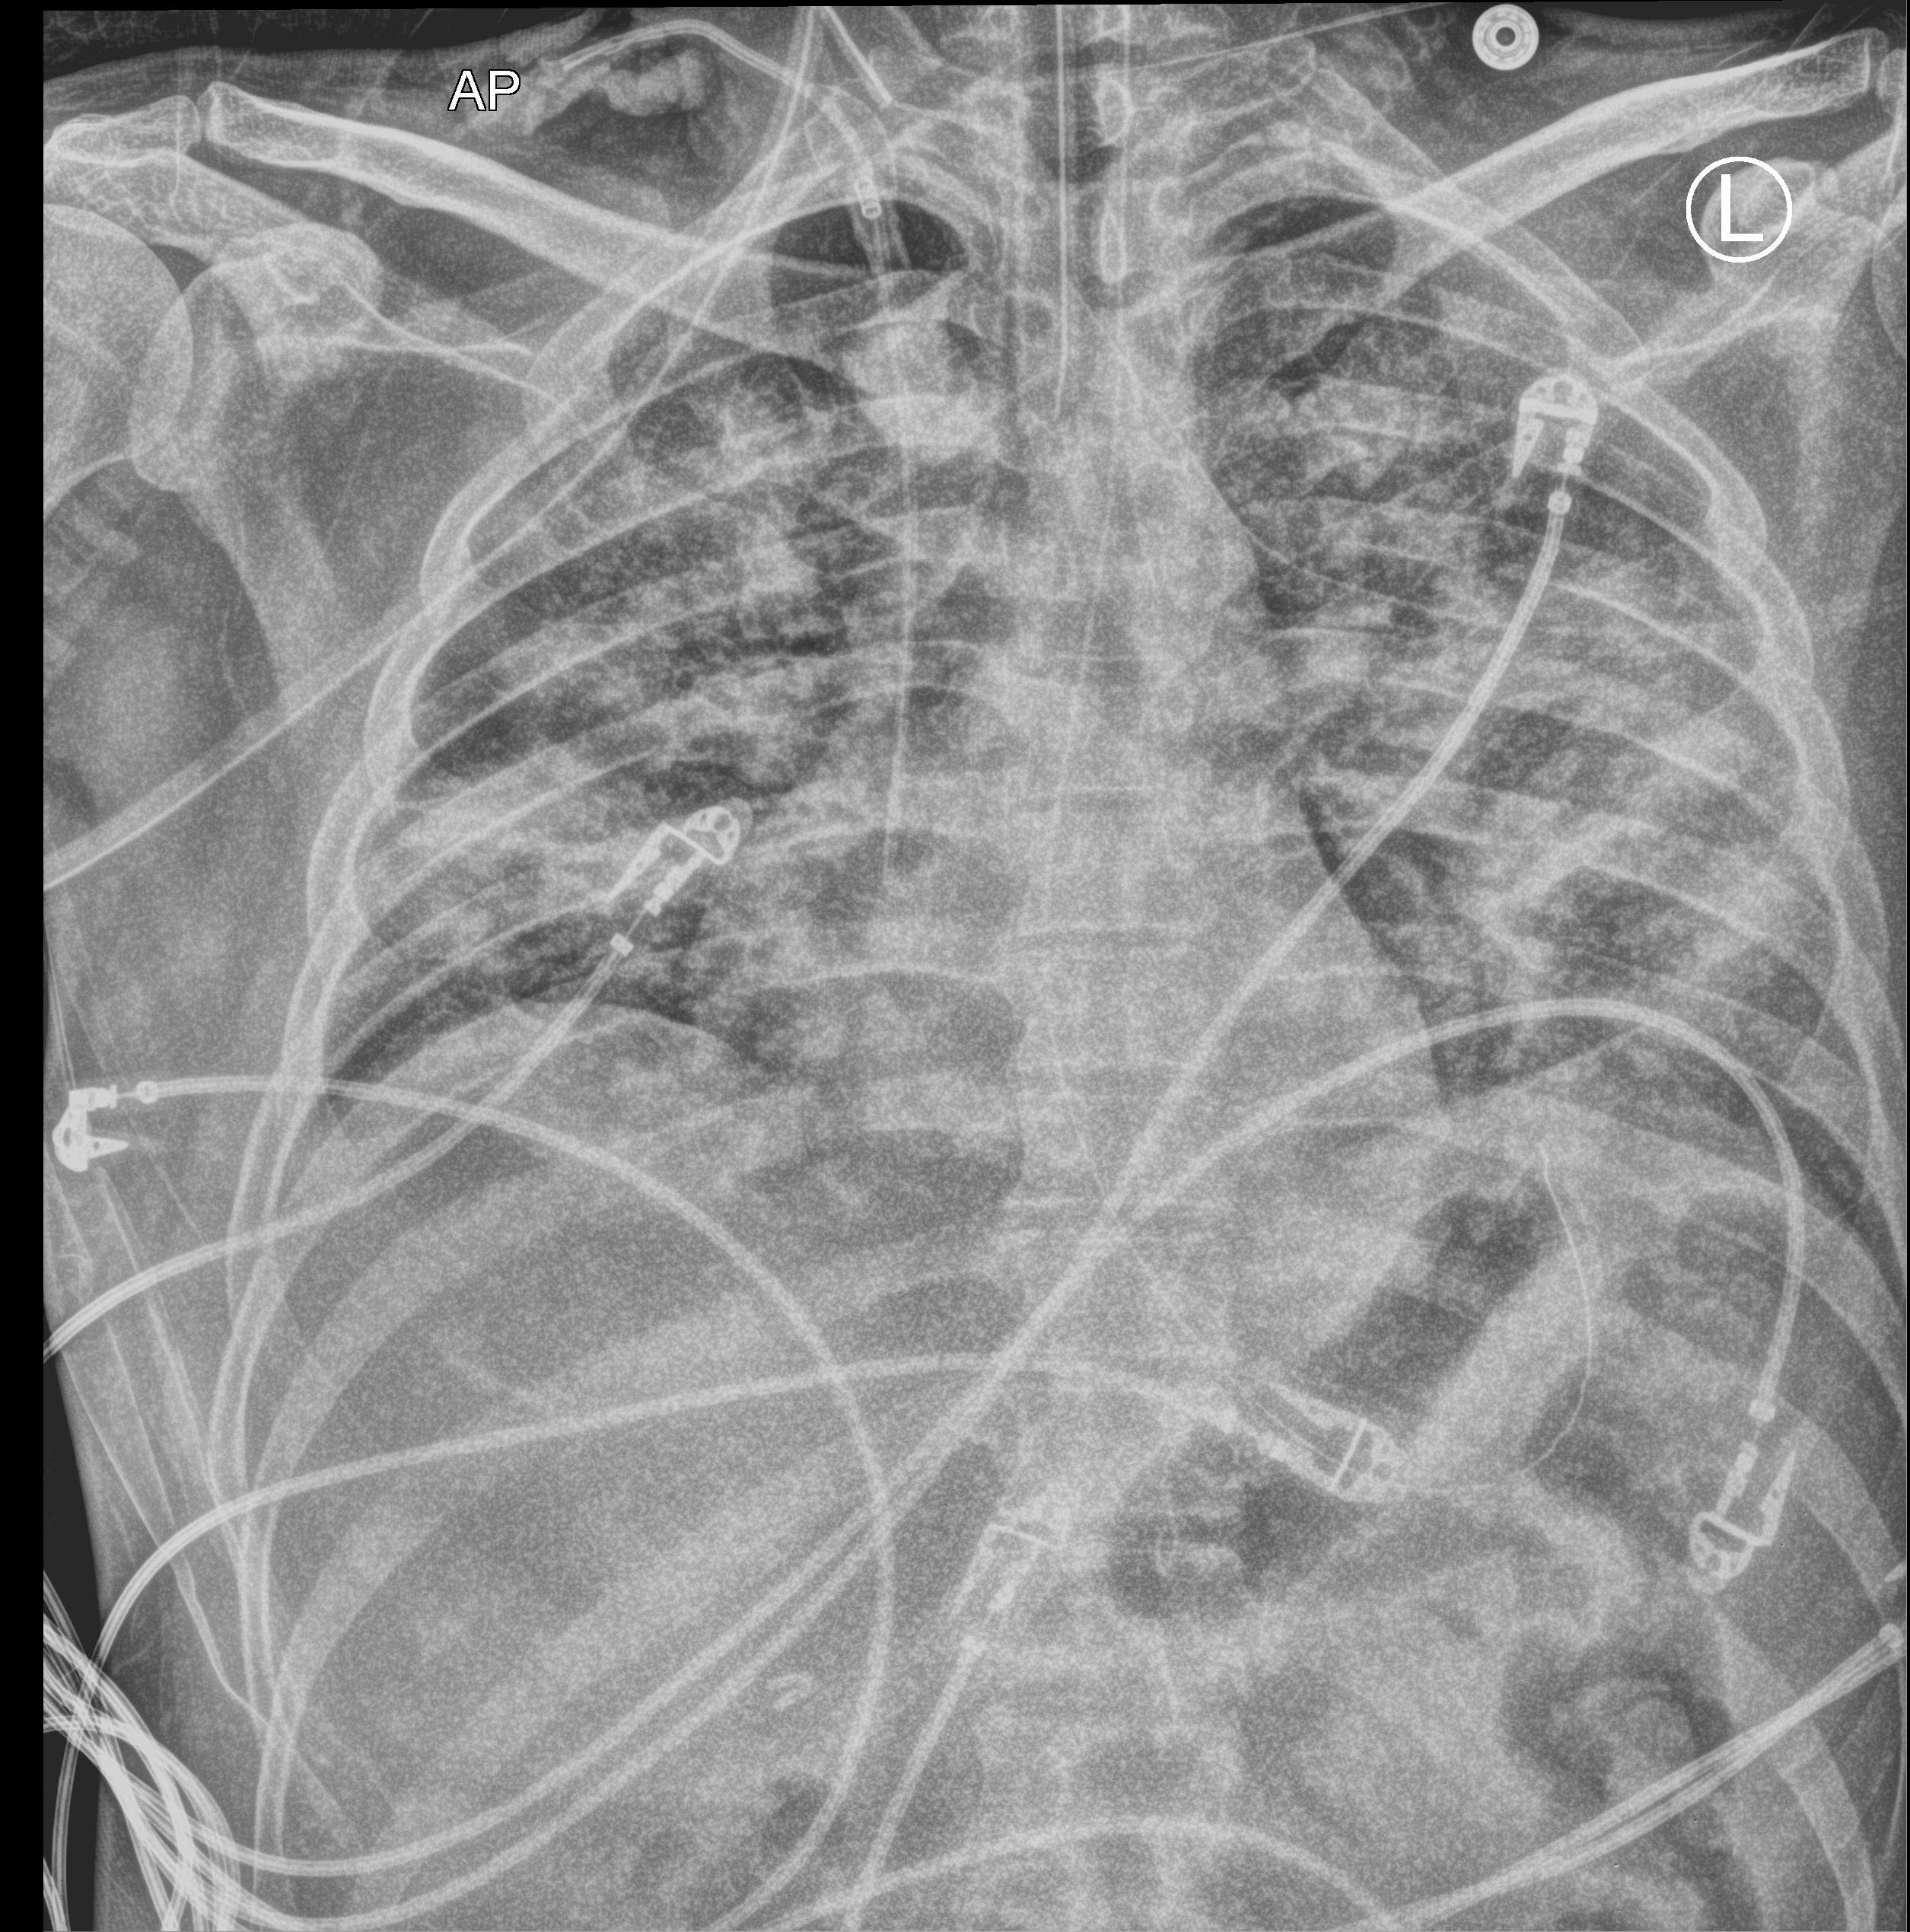
Chest X-ray (portable); anteroposterior (AP) projection. Male patient hospitalised with COVID-19, age 18–59 years.
Hospital-stay facts (about this admission, not read from this image; timing relative to this image not recorded):
- mechanically ventilated during this hospital stay: yes
- admitted to intensive care during this hospital stay: yes